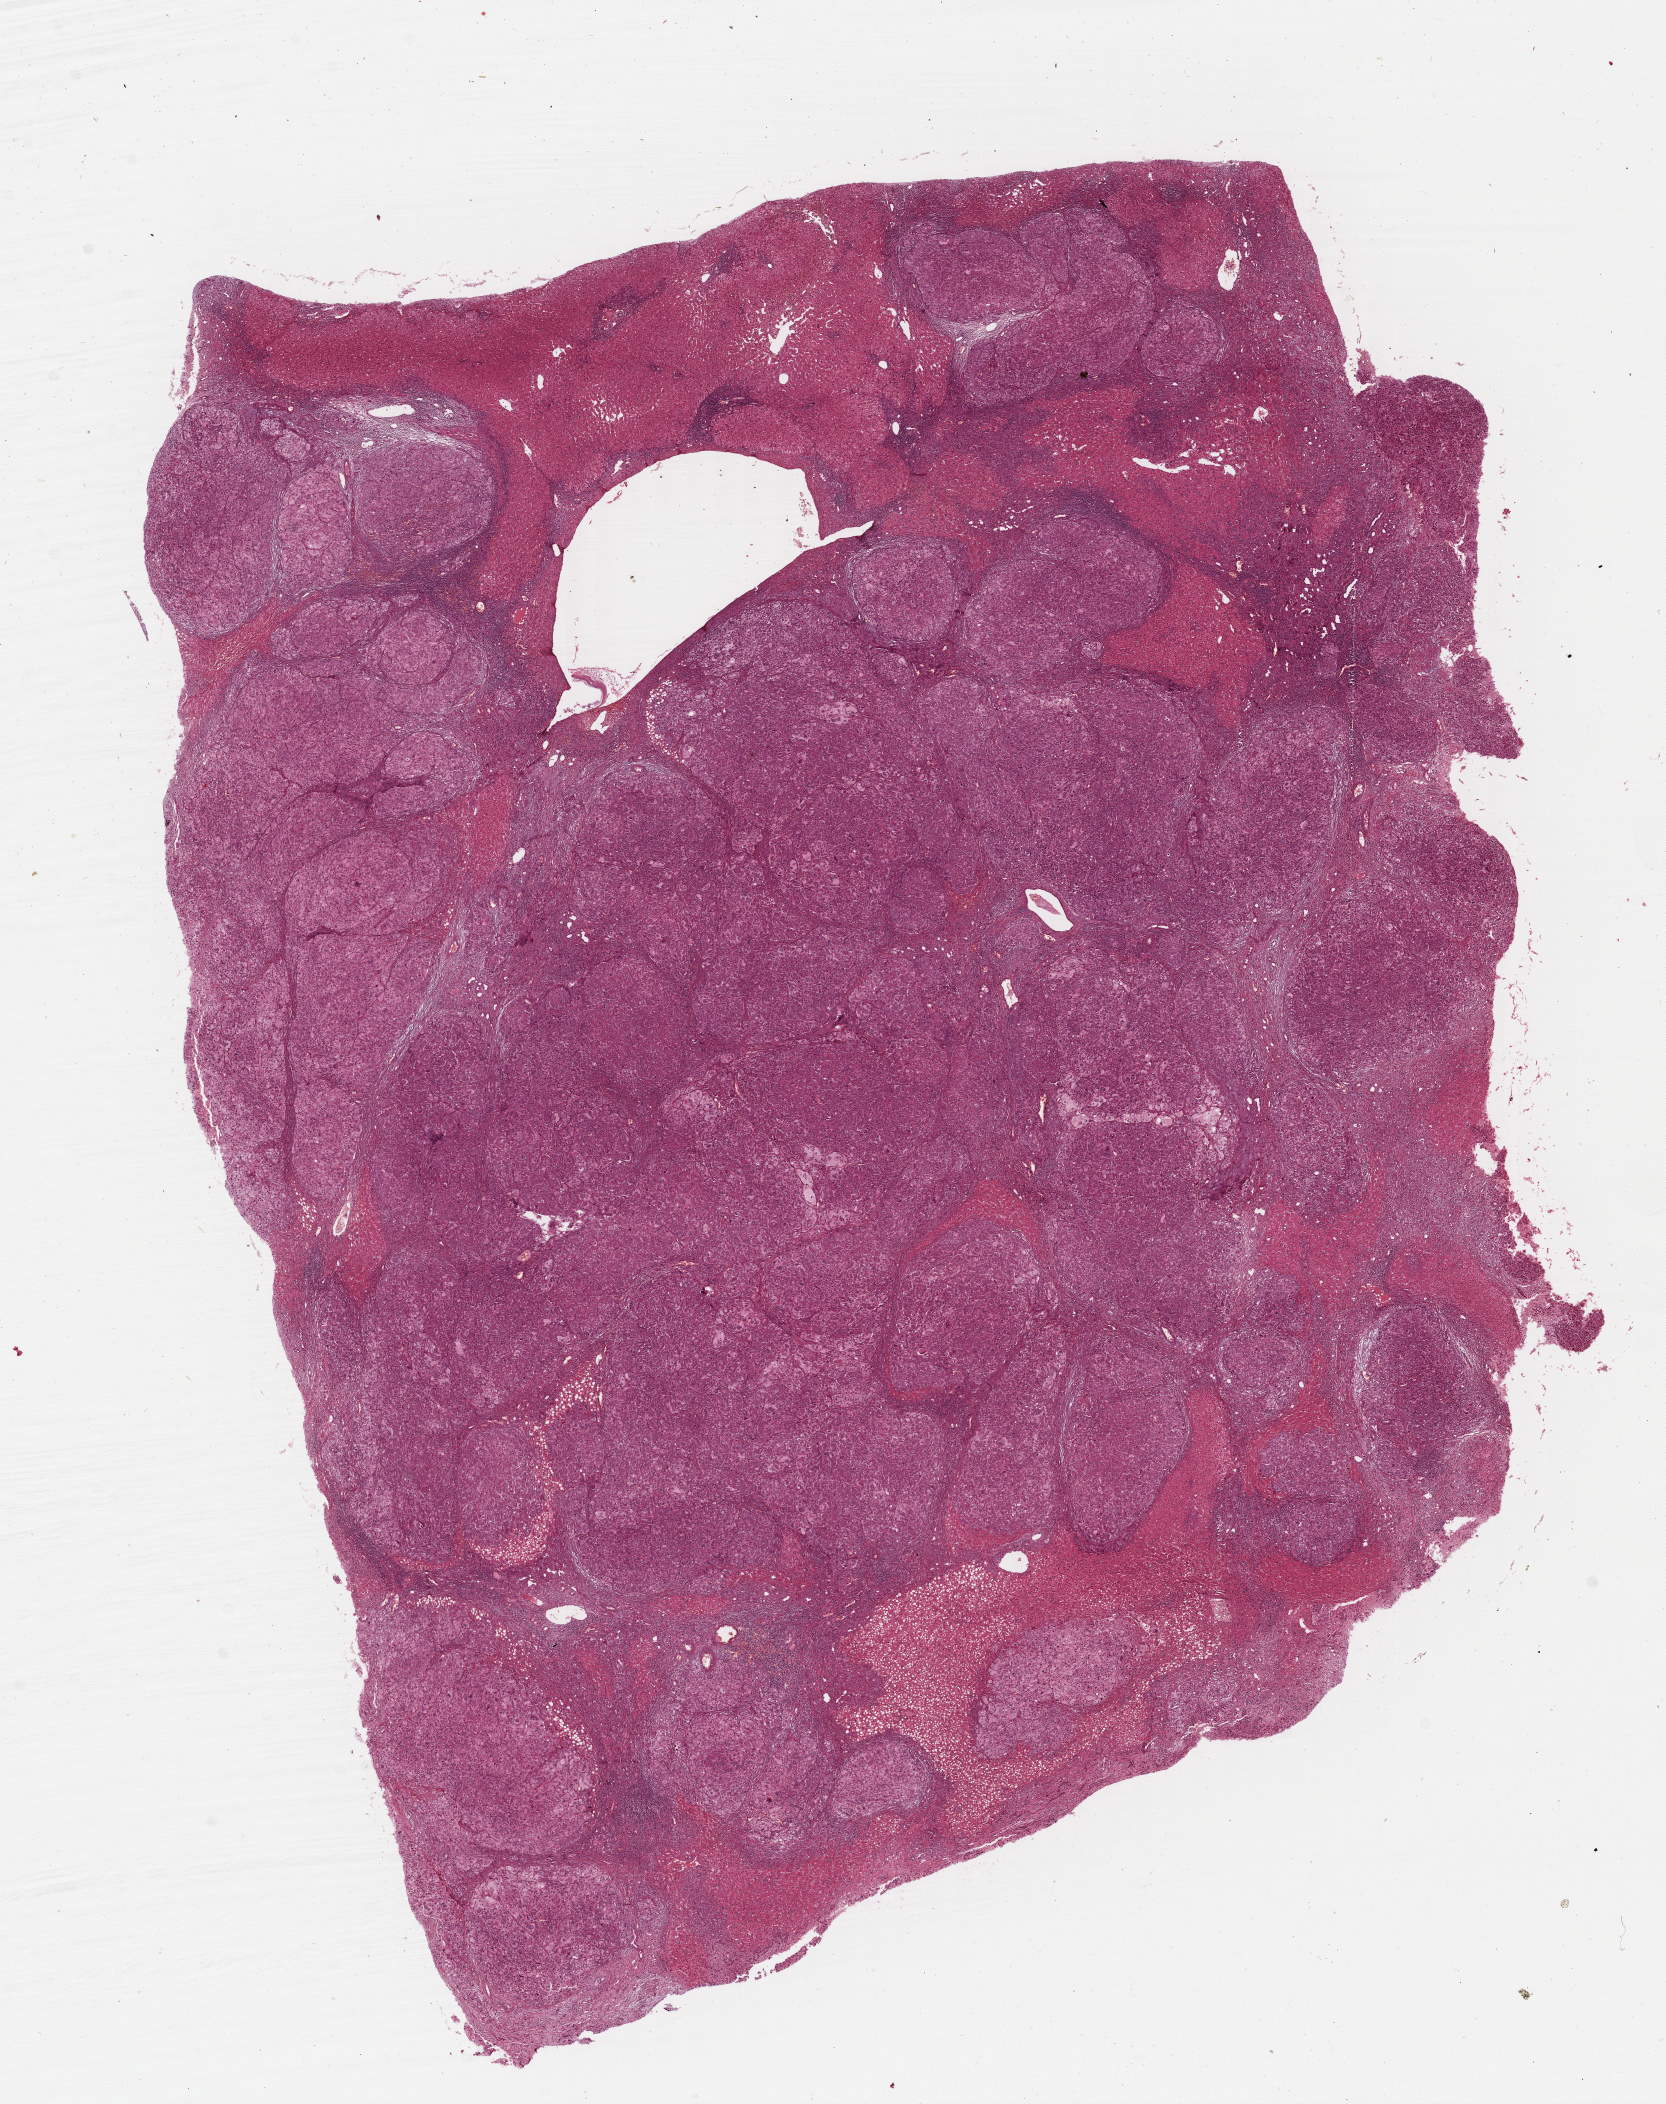
H&E-stained whole-slide image — a low-resolution overview of the entire scanned area, about 13.1 x 16.5 mm (slide scanned at 40x), formalin-fixed paraffin-embedded (FFPE) diagnostic section, primary tumour sample from the liver. Male patient; age at initial diagnosis 63 years. Histologic grade: G3 (poorly differentiated).
- AJCC pathologic stage: IIIA (6th edition)
- diagnosis: Hepatocellular carcinoma, NOS